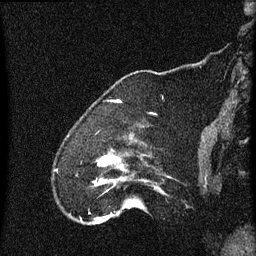
Breast MRI (dynamic contrast-enhanced), one sagittal slice; slice 11 of 60 in the series (ordered by position); dynamic contrast-enhanced series, image 2 of 4 at this slice position (ordered by acquisition); 1.5 T; TE 4.2 ms, TR 8 ms; 2 mm slice thickness; 256 × 256 image matrix, field of view 180 × 180 mm. Patient: female, 52 years.
Annotated regions visible in this slice (semi-automatically segmented with operator editing):
- analysis volume of interest (the breast-tissue region the enhancement analysis was run in; not a lesion): box from (x=73, y=148) to (x=166, y=219) px
- tumour enhancement mask (voxels above the 70 % enhancement threshold inside the analysis volume of interest): (x=94, y=156)–(x=112, y=183)